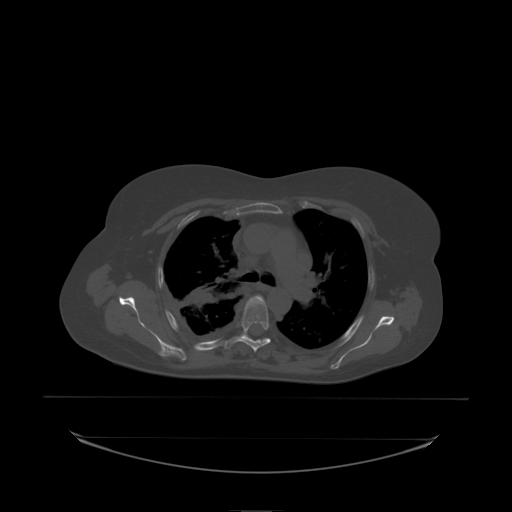
CT including the spine, one axial slice. Position 159 of 242 along the scan axis. Bone window (W 1800 / L 400 HU). 512 × 512 image matrix. Female patient, age 53 years. Case-level facts recorded for this patient, not image findings: primary cancer: lung.
Annotated regions visible in this slice (semi-automatically segmented with operator editing):
- T4 vertebra: box from (x=247, y=296) to (x=263, y=305) px
- T5 vertebra: (x=242, y=298)–(x=269, y=338)